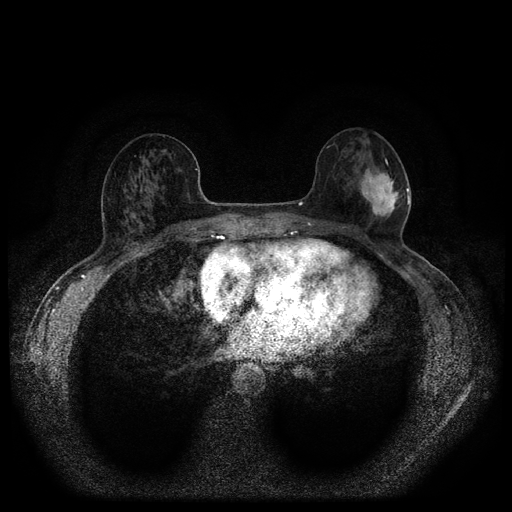
Breast MRI (dynamic contrast-enhanced, multi-phase), one axial slice; position 47 of 116 along the scan axis; dynamic contrast-enhanced series, time point 2 of 5 at this slice position (early post-contrast); 1.5 T; TE 2.7 ms, TR 5.4 ms; 2 mm slice thickness; 512 × 512 image matrix, field of view 330 × 330 mm. Patient: female, 56 years.
Structures marked on this image (semi-automatic segmentation, software-assisted and operator-edited):
- breast lesion (labelled 'tumour' in the annotation; benign lesions carry a separate 'benign' label): bounding box (x1, y1, x2, y2) in pixels: (359, 166, 401, 221)